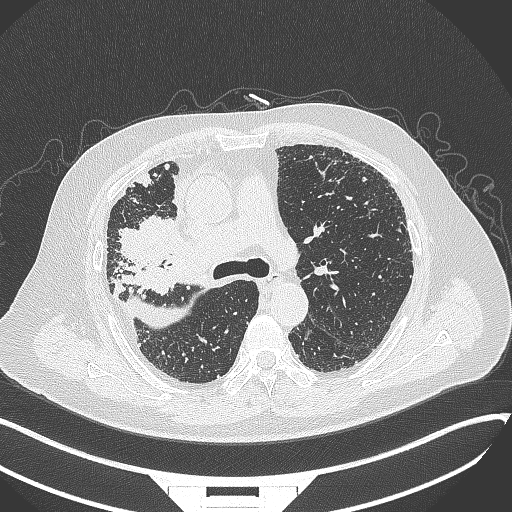
Chest CT, one axial slice; position 221 of 384 along the scan axis; reconstruction kernel B70f; lung window (W 1500 / L -600 HU); 512 × 512 image matrix, field of view 400 × 400 mm. Patient: male, 69 years. From the clinical record (not read from this slice): clinical TNM (as recorded): T4 N3 M1.
Structures marked on this image (bounding box drawn by a radiologist):
- lung tumour (recorded histology: adenocarcinoma): bounding box <115,215,183,272> (left, top, right, bottom; pixels)